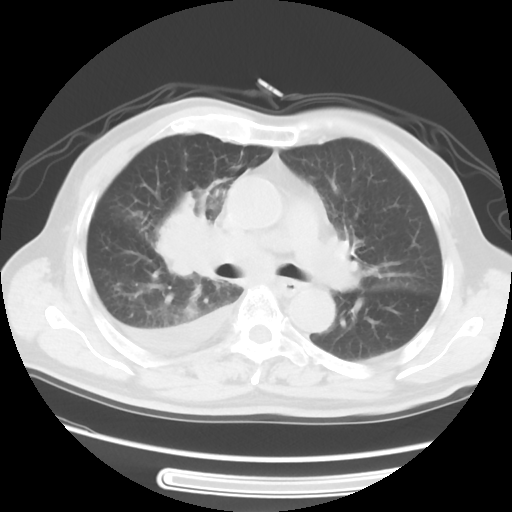
Chest CT, one axial slice. Slice 33 of 56 in the series (ordered by position). Reconstruction kernel STANDARD. 120 kVp. Lung window (W 1500 / L -600 HU). 5 mm slice thickness. 512 × 512 image matrix, field of view 360 × 360 mm. Patient: male, 77 years. Case-level facts recorded for this patient, not image findings: clinical TNM (as recorded): T3 N3 M1b; histopathological grade: G3.
Structures marked on this image (bounding box drawn by a radiologist):
- lung tumour (recorded histology: small cell carcinoma): bounding box (x1, y1, x2, y2) in pixels: (150, 195, 221, 288)